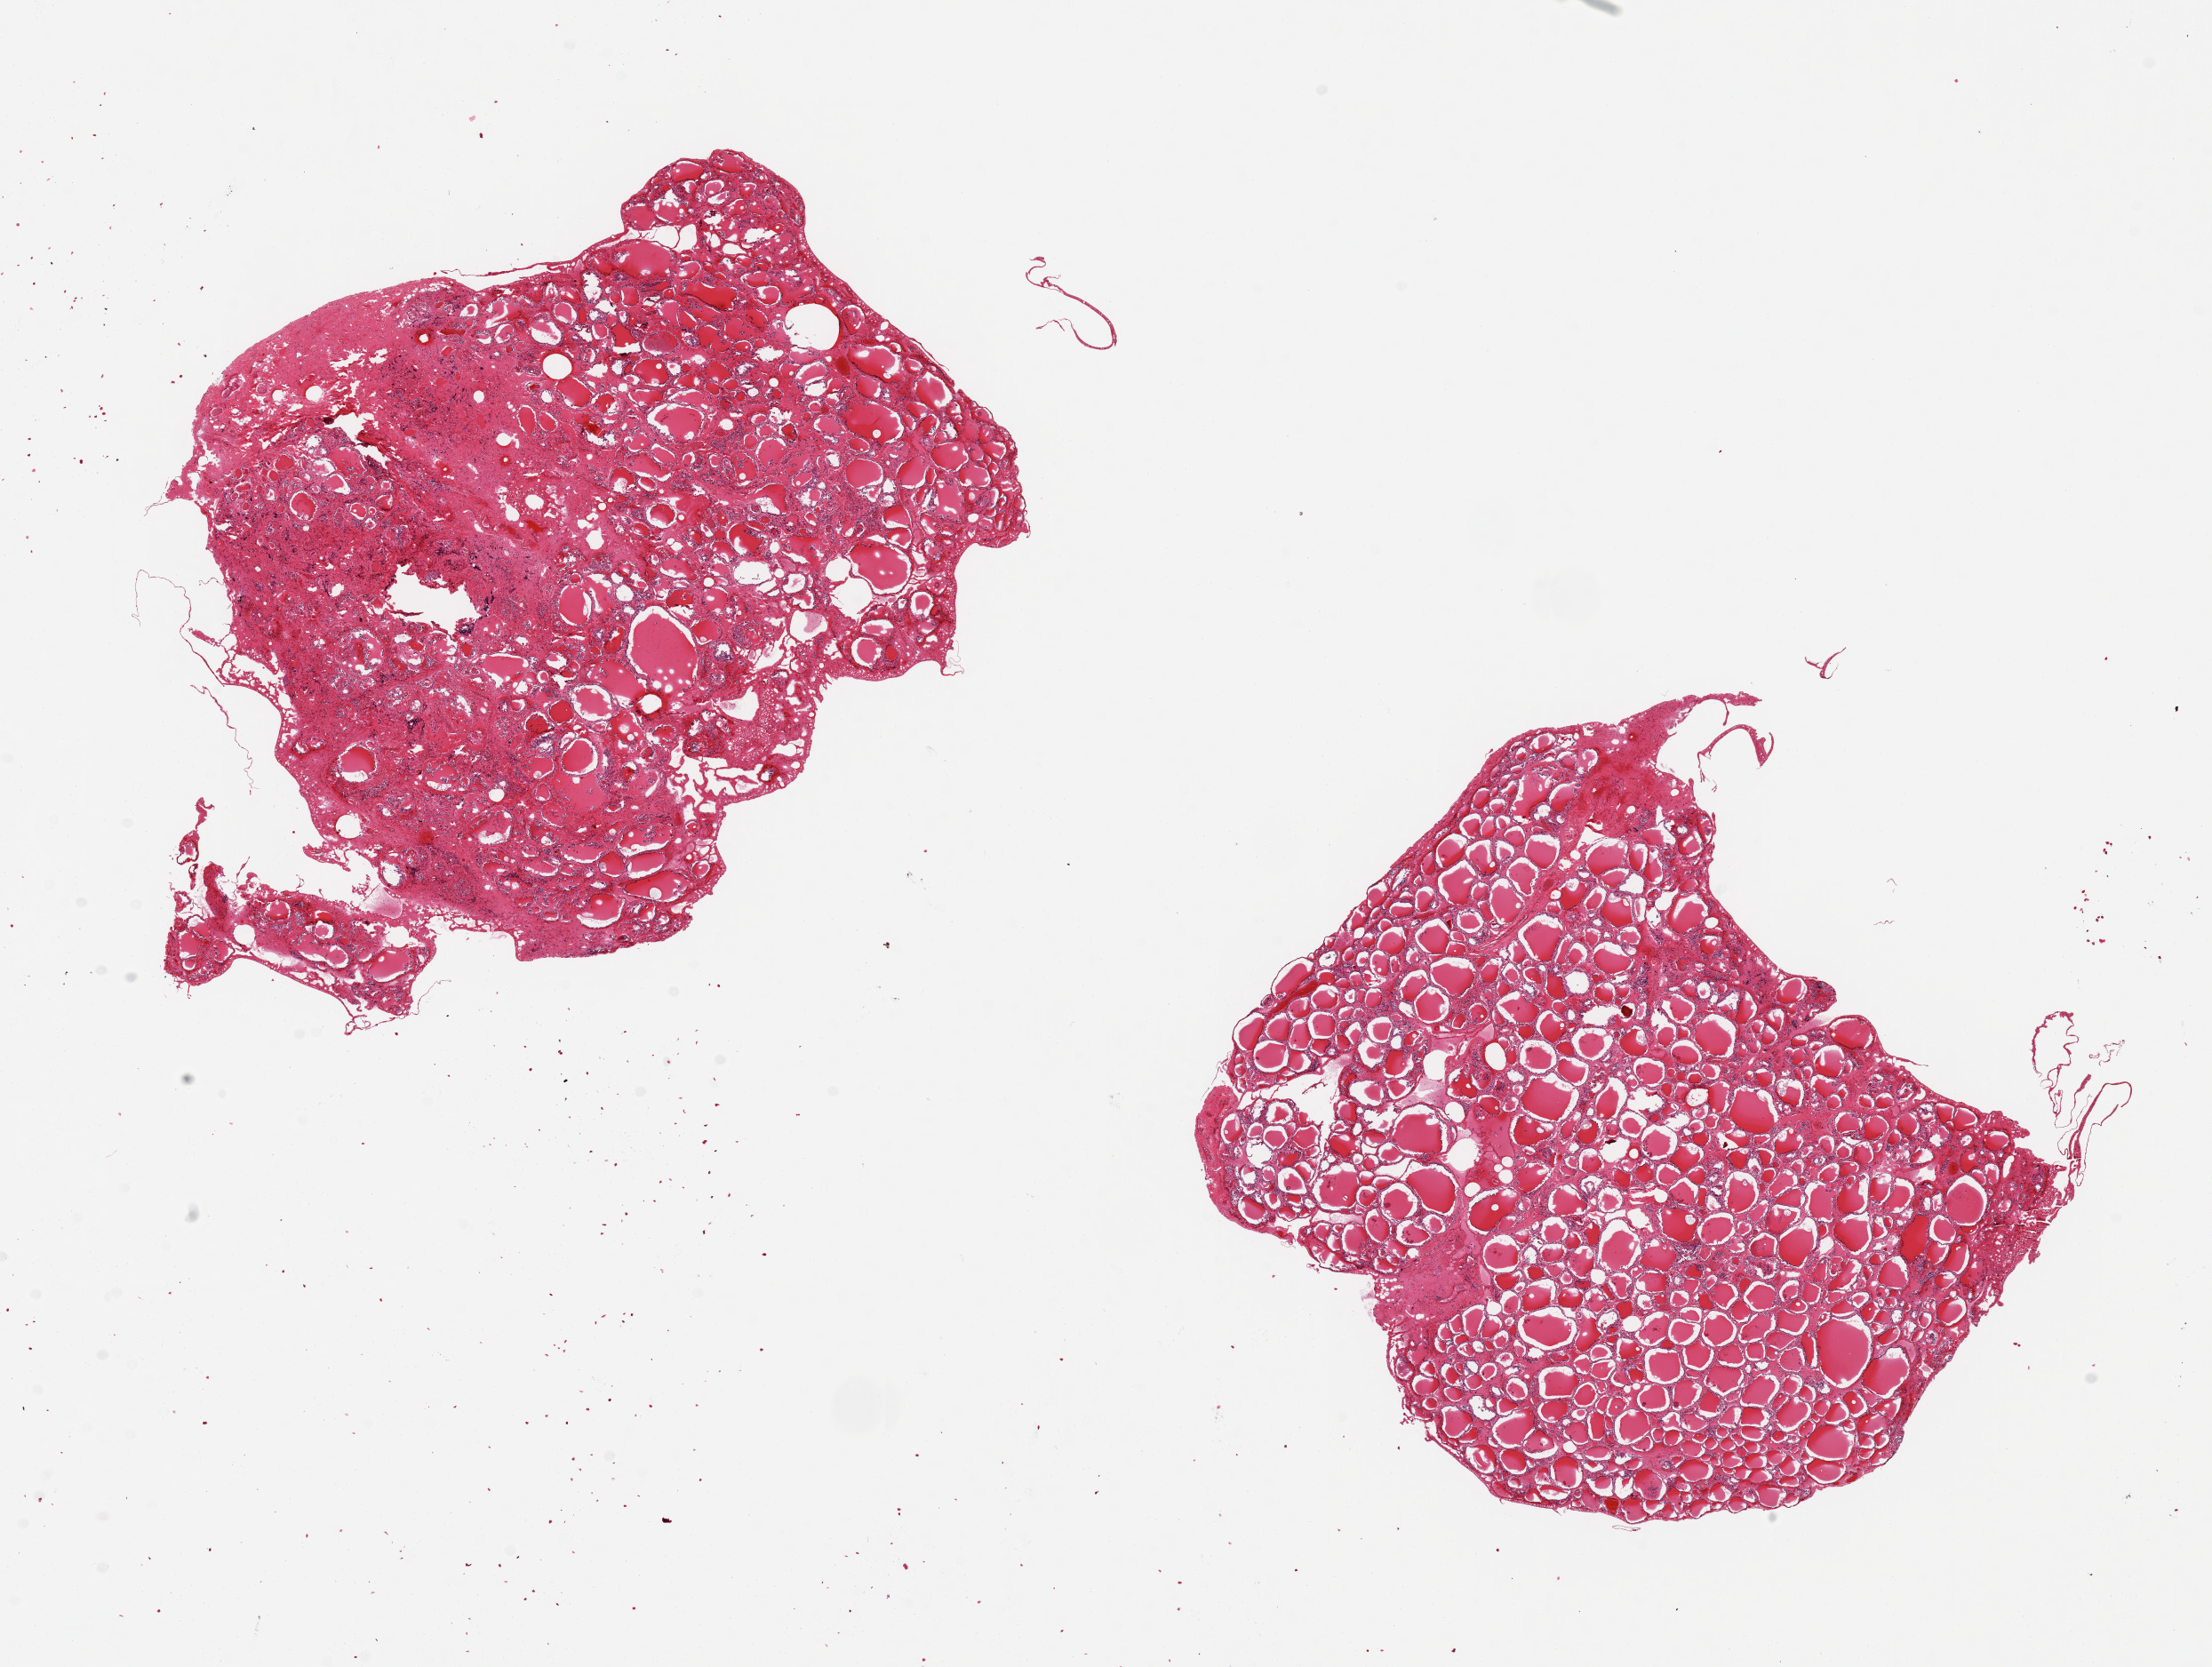
Haematoxylin and eosin whole-slide image, a low-resolution overview of the entire scanned area, about 19.7 x 14.8 mm; PAXgene-fixed, paraffin-embedded tissue; section of thyroid (target tissue); tissue donor sample. Donor sex: male.
Reviewer comment on this tissue sample: 2 pieces 6x5 & 7x6 mm.